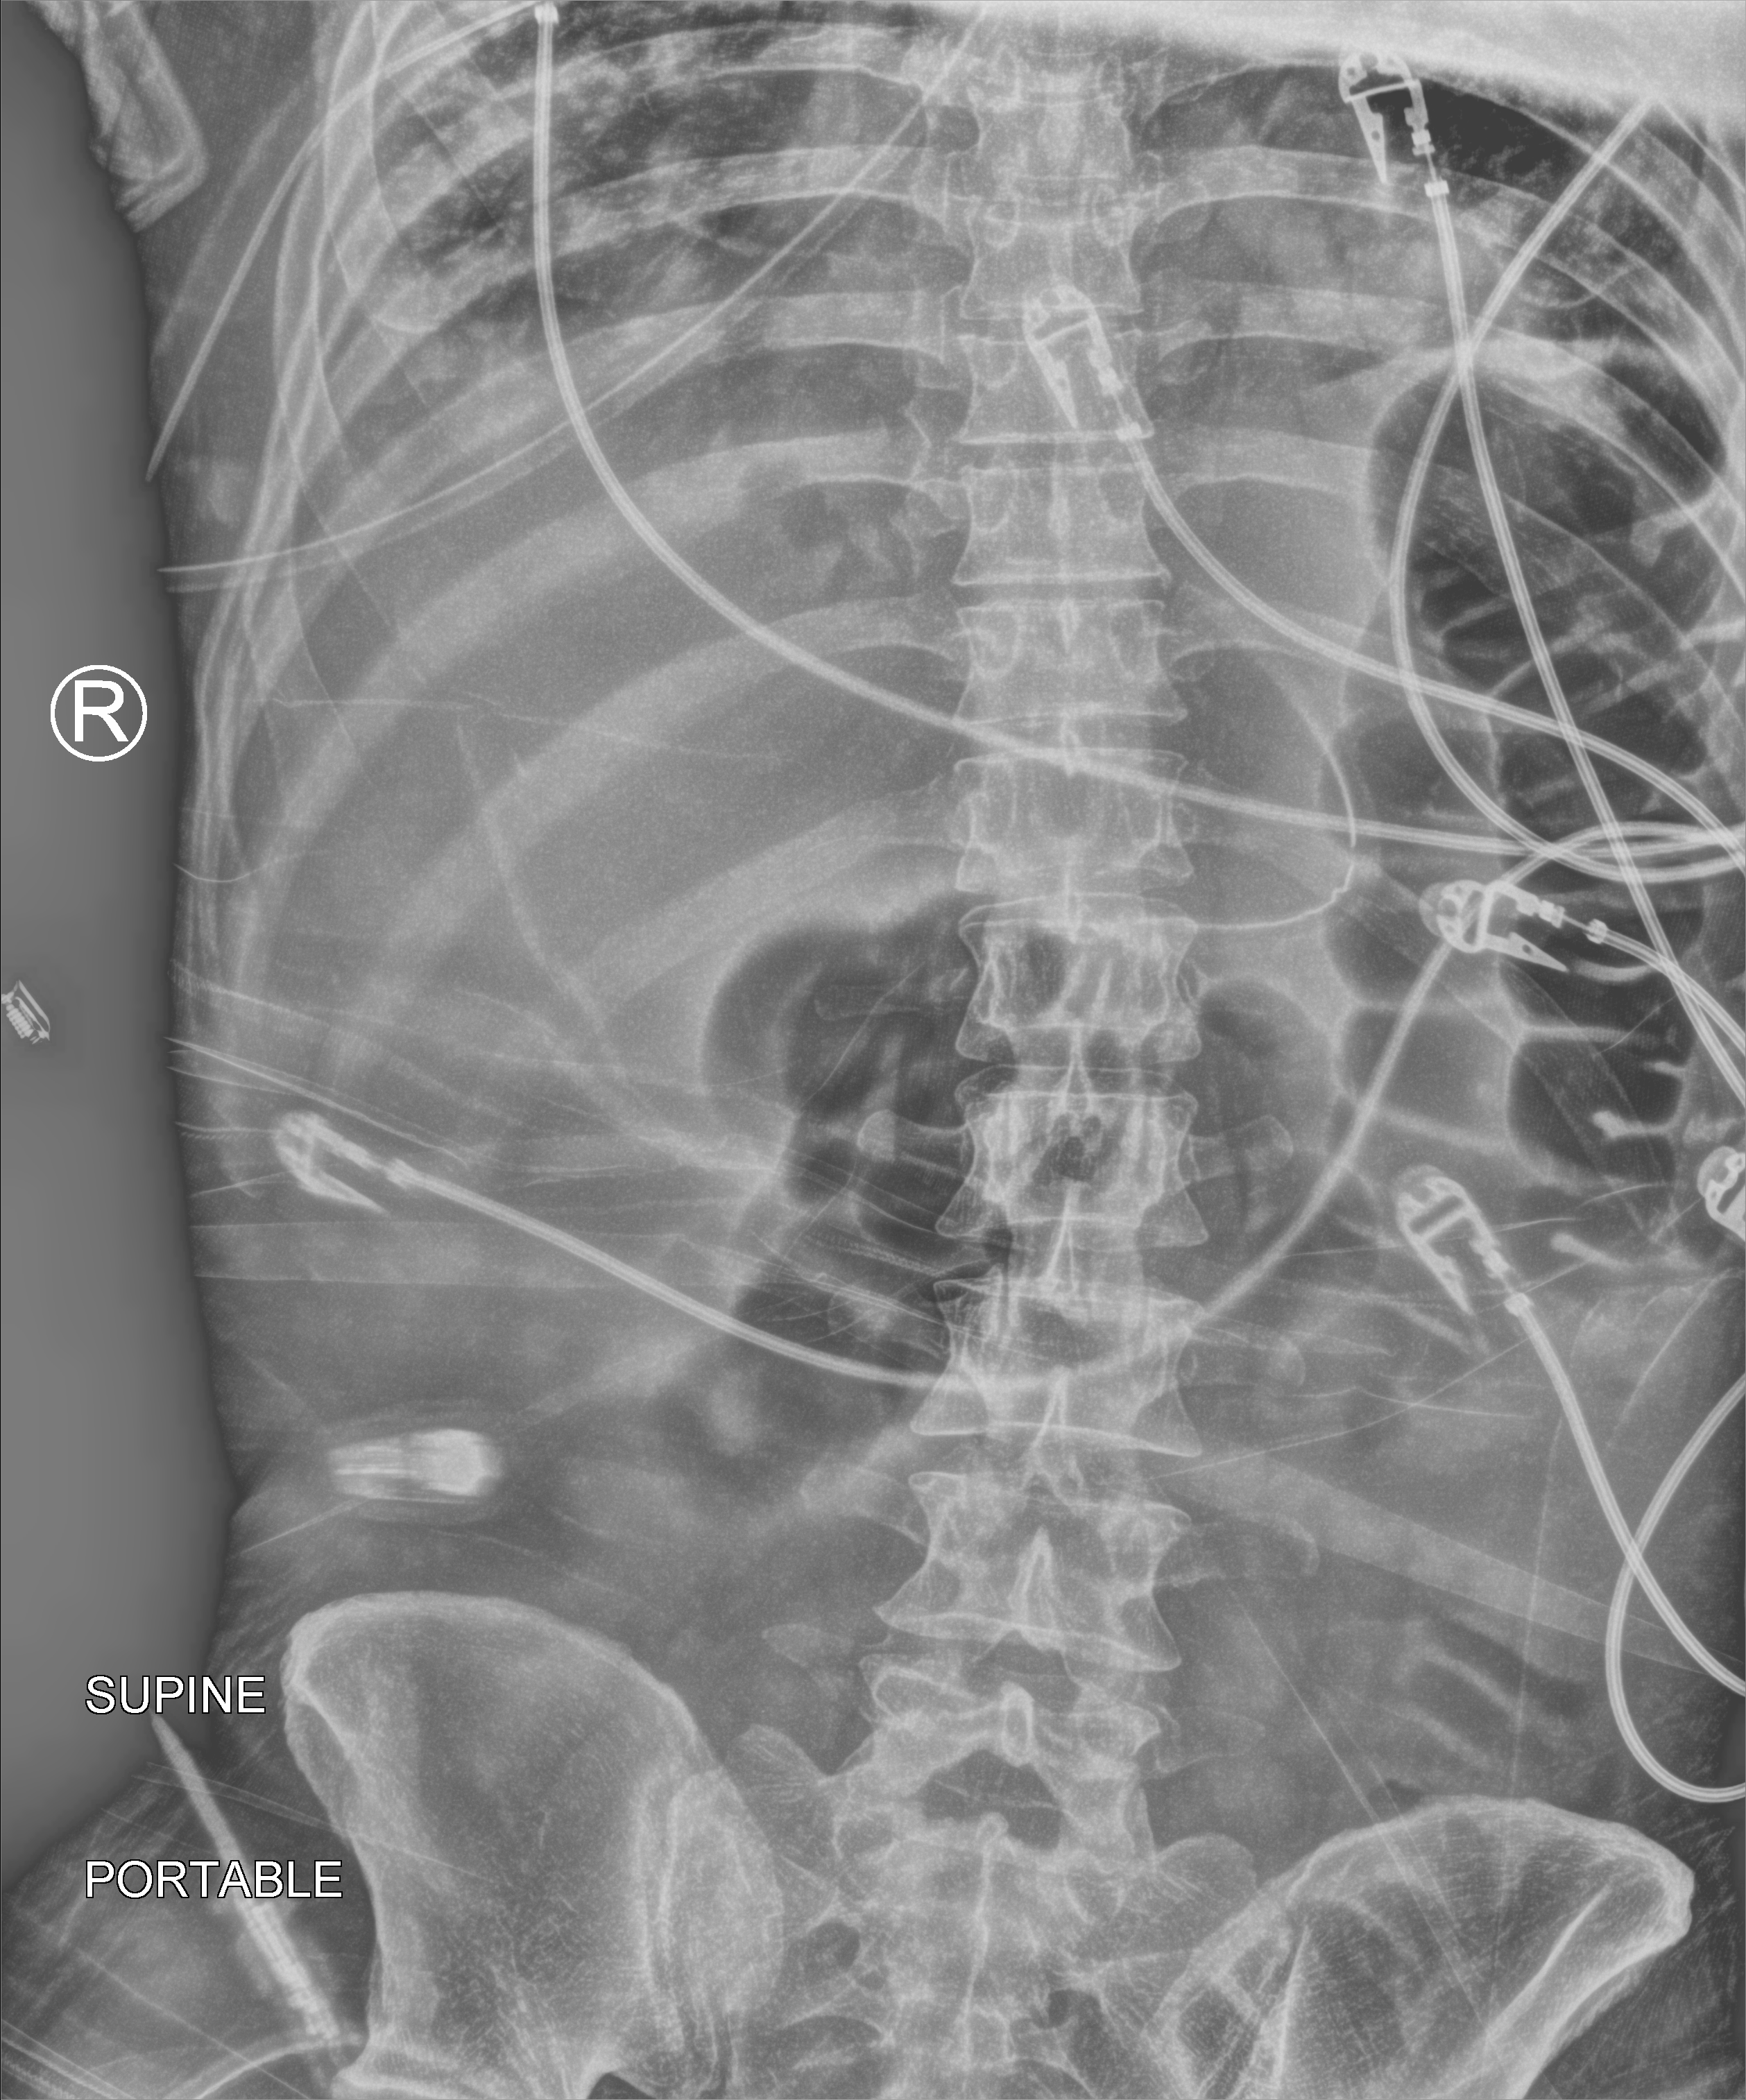
Abdomen X-ray (portable), anteroposterior (AP) projection. Male patient hospitalised with COVID-19, age 18–59 years.
Hospital-stay facts (about this admission, not read from this image; timing relative to this image not recorded): chronic kidney disease (admission record): no; mechanically ventilated during this hospital stay: yes.